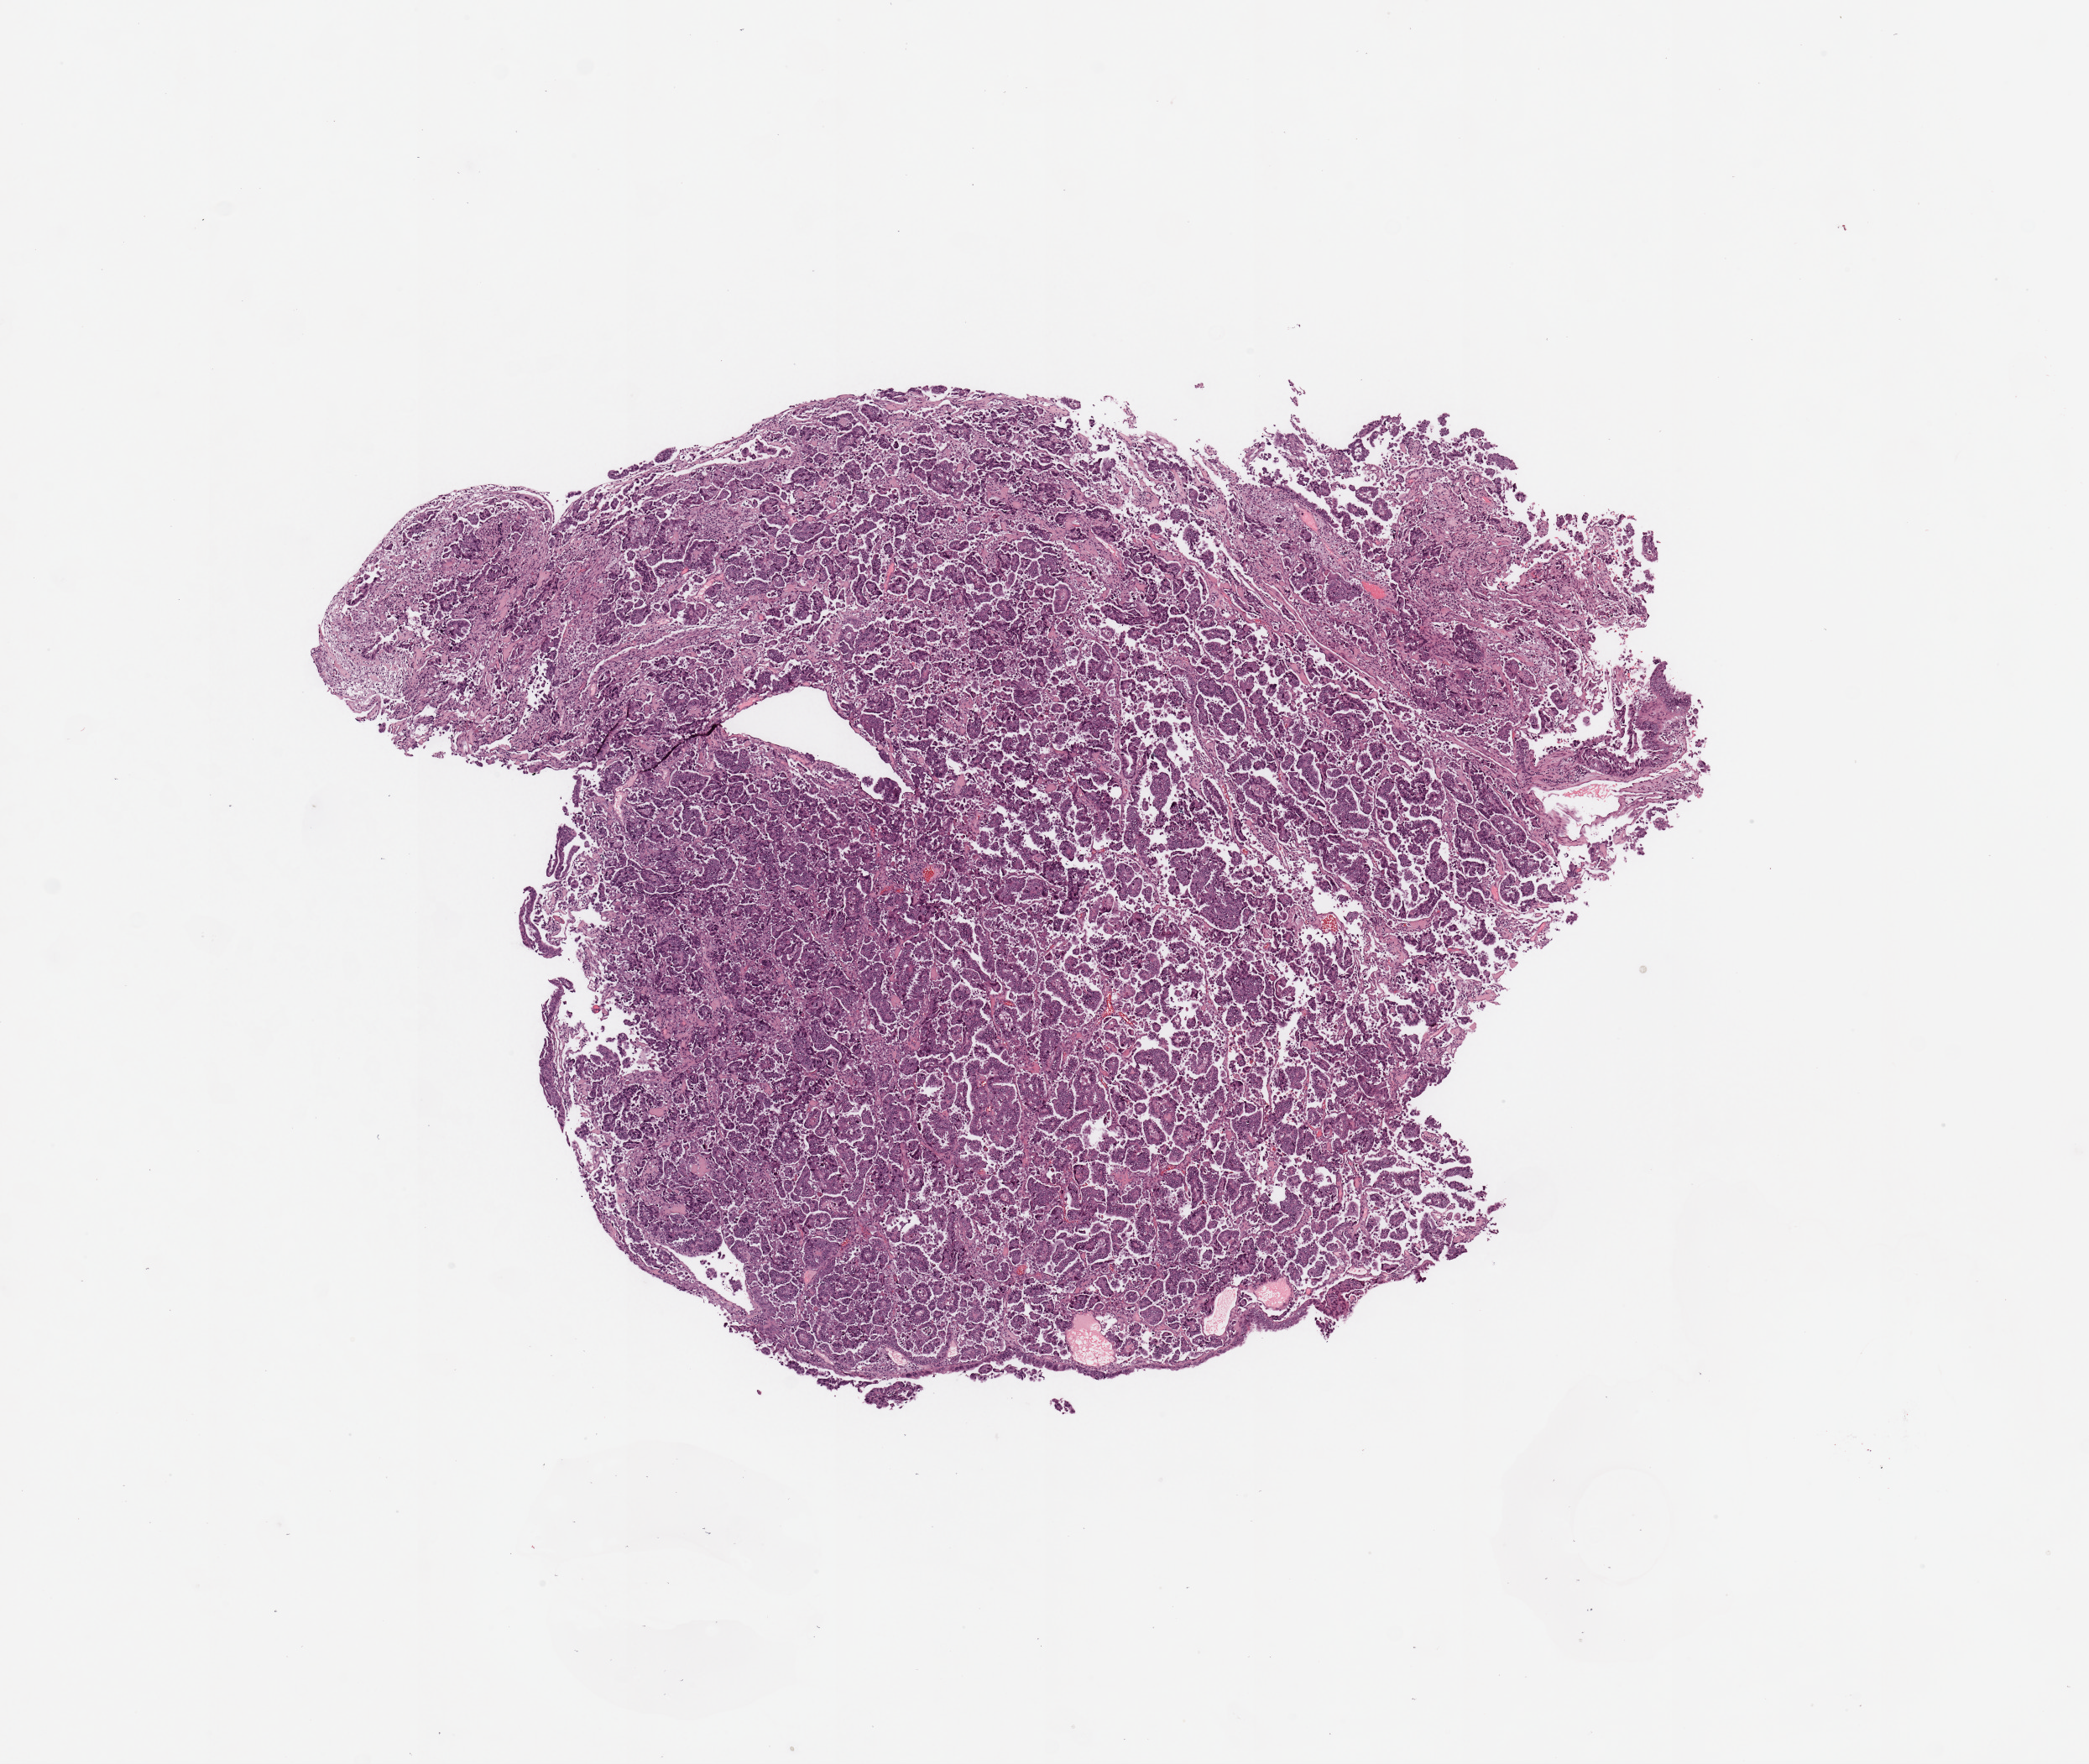
Digitized H&E-stained tissue section (whole slide), a low-resolution overview of the entire scanned area, about 9.8 x 8.3 mm (from a 20x scan); tumour tissue sample, sampled site: uterus. 67-year-old female patient. Composition of this section per pathologist review: tumour nuclei 80%, necrosis 0%.
* diagnosis: Endometrioid adenocarcinoma, NOS
* AJCC pathologic stage: IVB